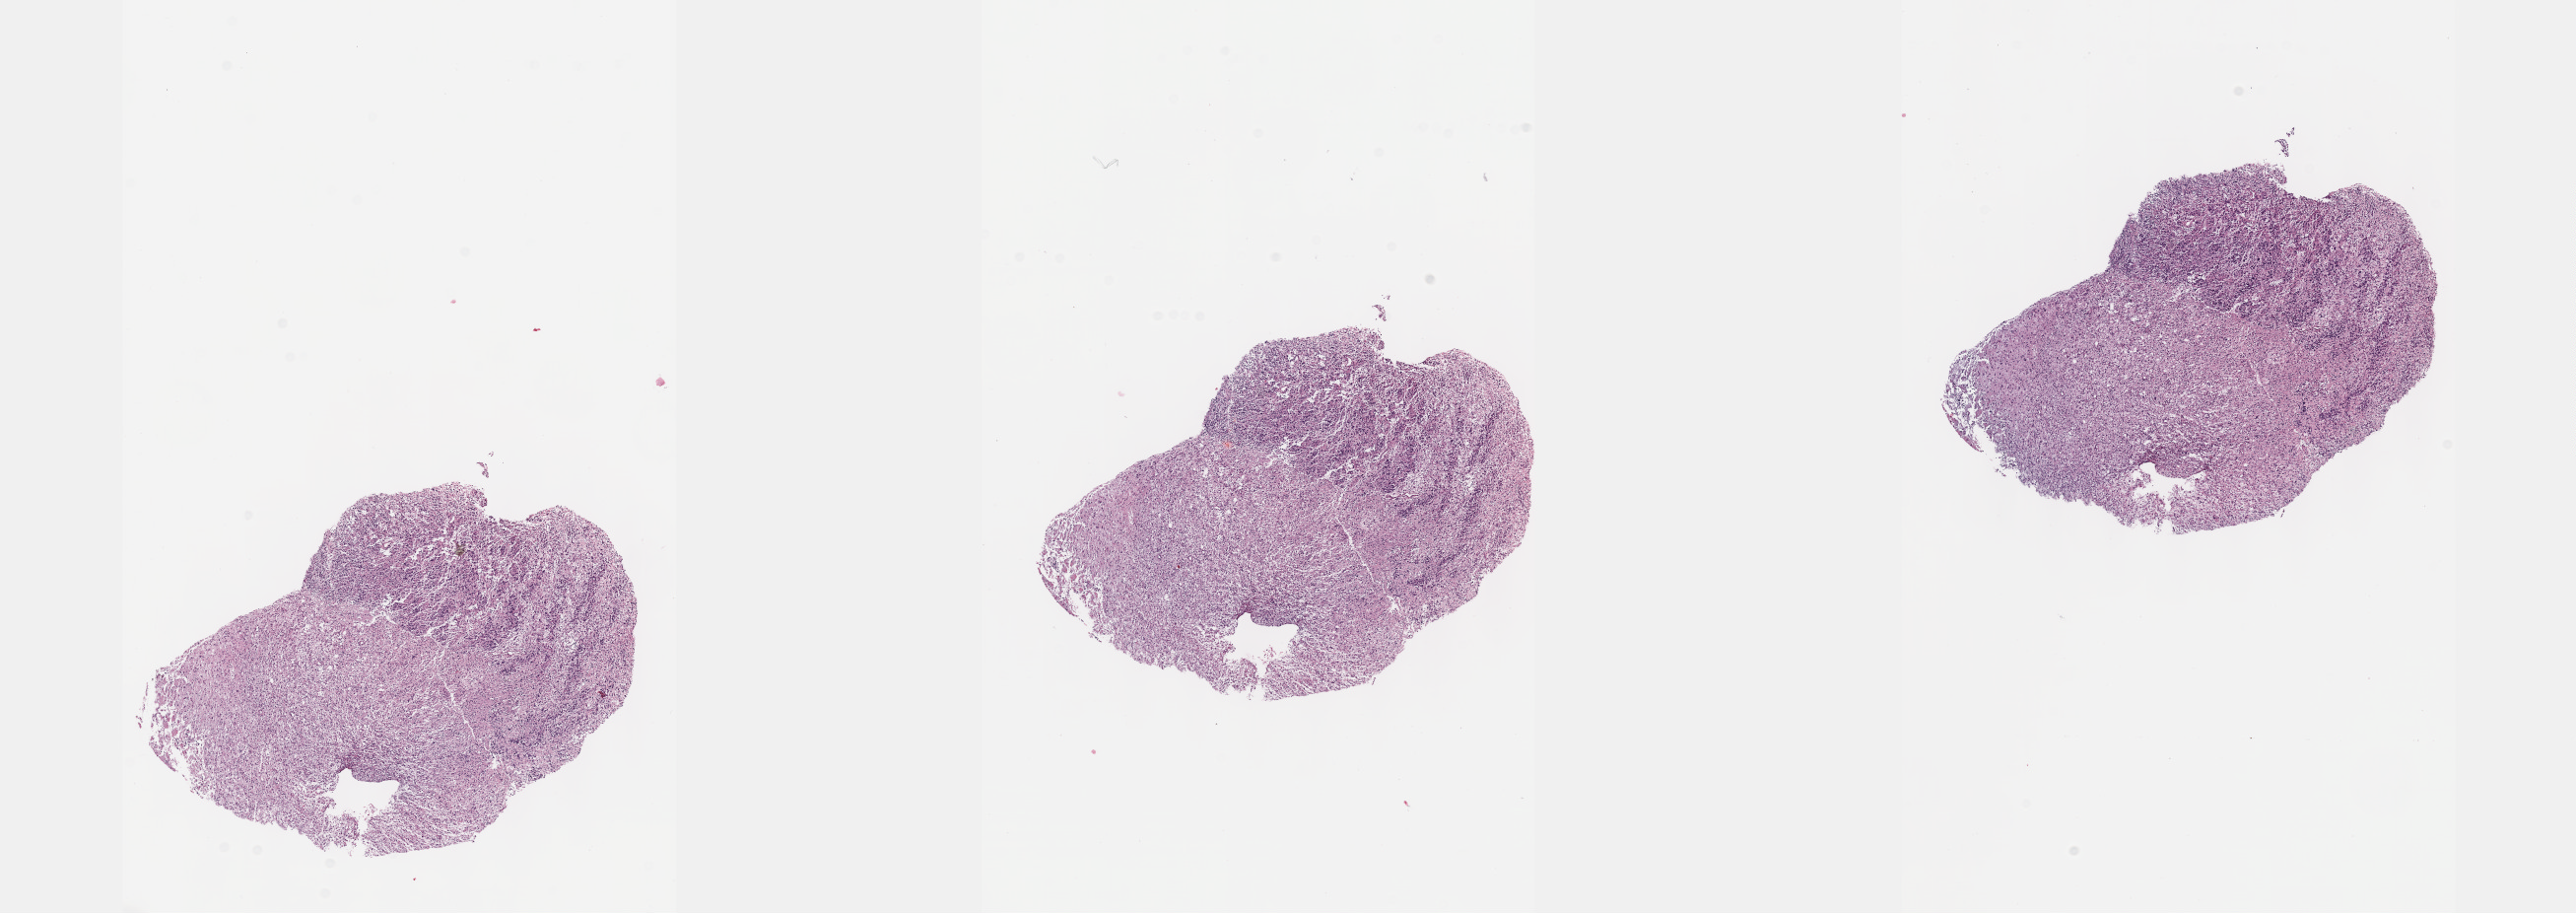
Digitized H&E tissue section (whole slide) — shown as a low-resolution overview of the whole scanned area (about 21.1 x 7.5 mm, acquisition: 40x scan). Formalin-fixed paraffin-embedded (FFPE) diagnostic section. Primary tumour sample from the brain. Patient: female, age at initial diagnosis 38 years. Histologic grade: G3 (poorly differentiated).
* laterality: left
* pathologic diagnosis: Astrocytoma, anaplastic (cerebrum)